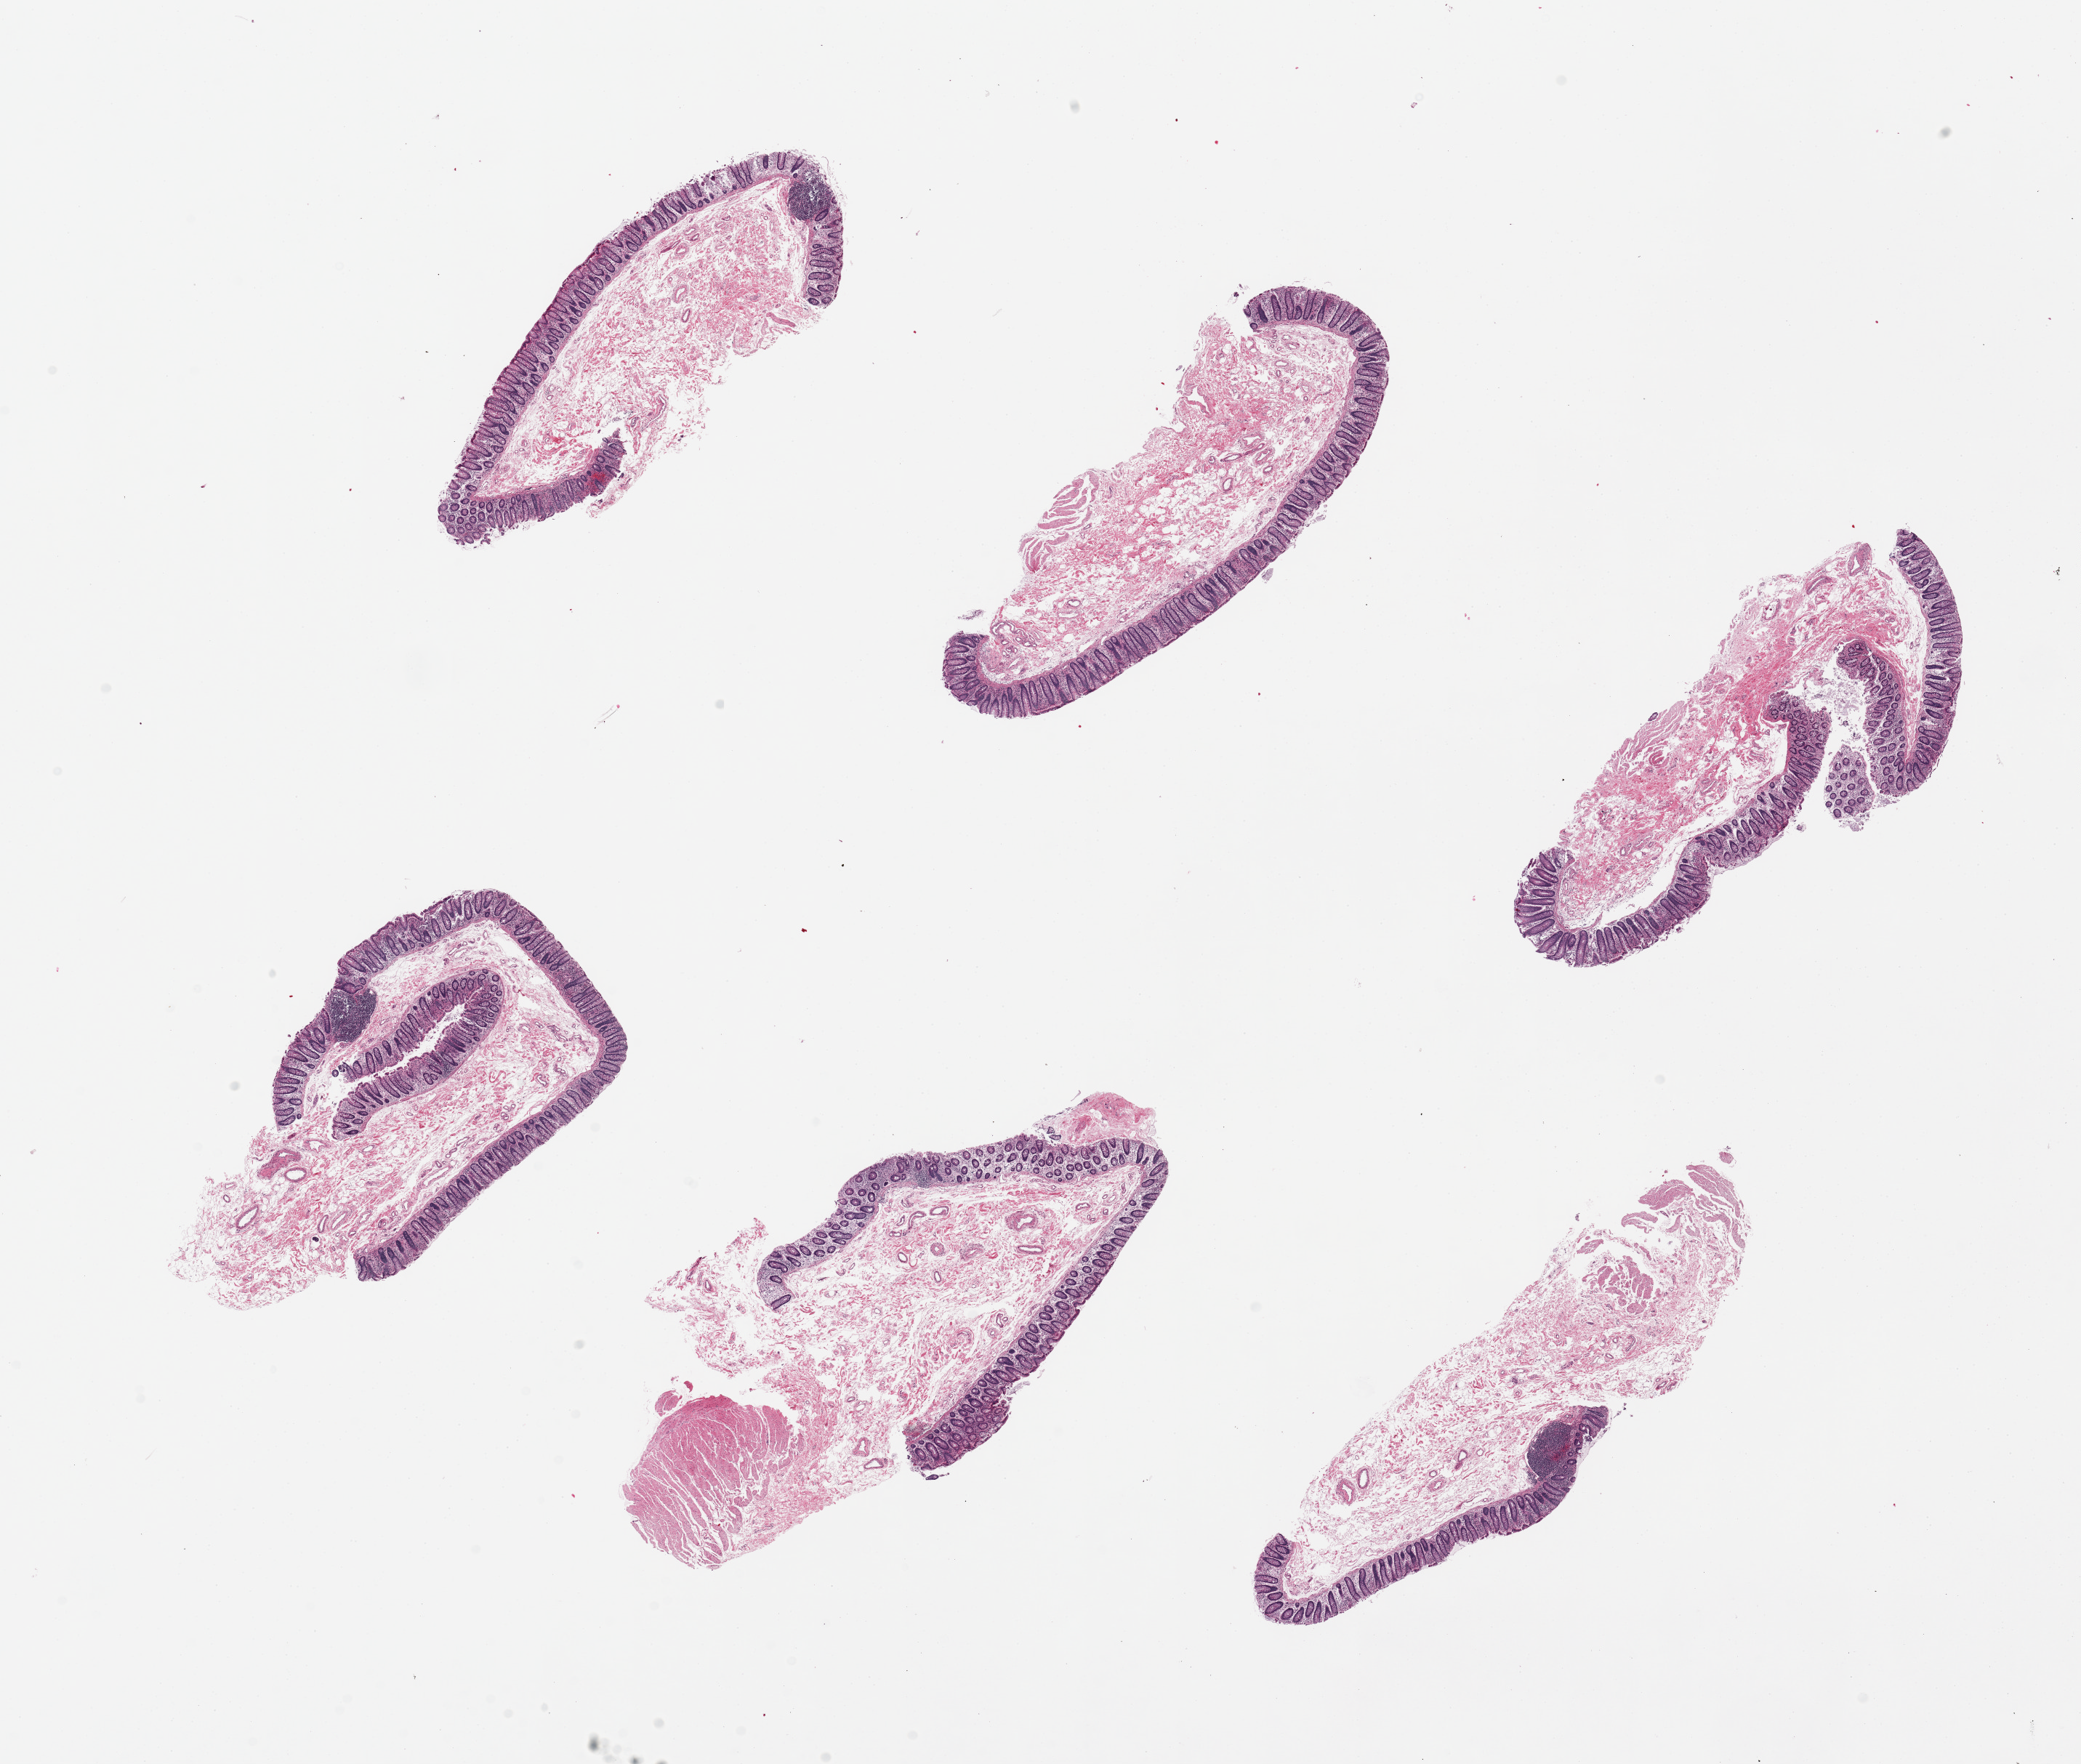
Whole-slide image, H&E stain — whole scanned area (about 22.6 x 19.2 mm, slide scanned at 20x) shown as a low-resolution overview. PAXgene-fixed paraffin-embedded (PFPE) section. Section of transverse colon (target tissue). Tissue donor sample. Male donor.
Reviewer comment on this tissue sample: 6 pieces, up to 7x2mm; only 1 of 6 has muscularis.